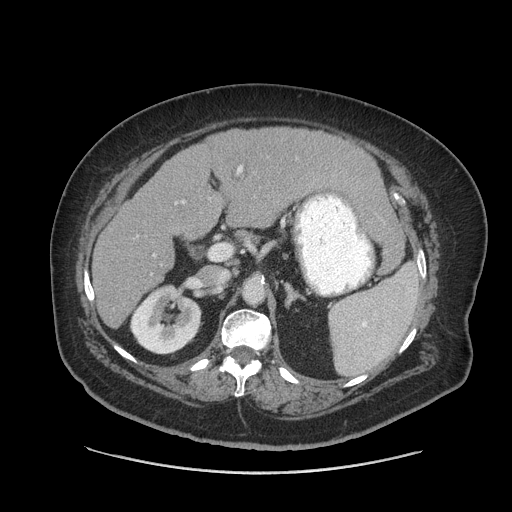
Contrast-enhanced abdominal CT (liver protocol), one axial slice; position 43 of 91 along the scan axis; soft-tissue window (W 400 / L 40 HU); 2.5 mm slice thickness; 512 × 512 image matrix, field of view 420 × 420 mm. Case-level facts recorded for this patient, not image findings: diagnosis: hepatocellular carcinoma (patient treated with transarterial chemoembolisation; whether this scan precedes or follows treatment is not stated here); TNM stage (as recorded): Stage-I; Child-Pugh class: A; tumour differentiation: well differentiated; tumour nodularity: uninodular.
Annotated regions visible in this slice (semi-automatic segmentation, software-assisted and operator-edited):
- liver parenchyma outside the tumour (the mass and vessels are separate outlines, so this box may not span the whole liver): box from (x=92, y=128) to (x=386, y=328) px
- liver vessels: (x=154, y=166)–(x=243, y=256)